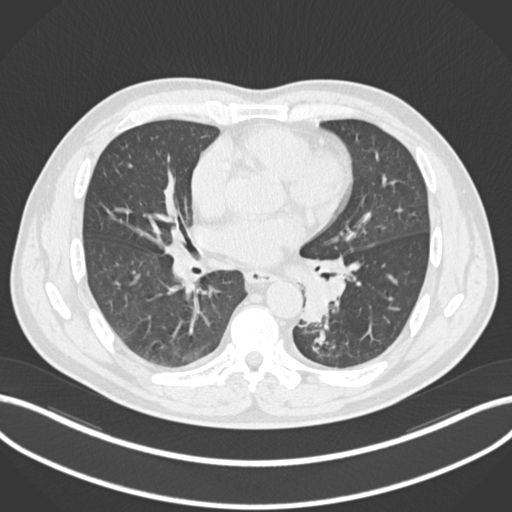
Chest CT, one axial slice. Slice 108 of 223 in the series (ordered by position). Reconstruction kernel B30f. 120 kVp. Lung window (W 1500 / L -600 HU). 512 × 512 image matrix. Patient: male, 50 years. Case-level facts recorded for this patient, not image findings: clinical TNM (as recorded): T2a N3 M0.
Annotated regions visible in this slice (bounding box drawn by a radiologist):
- lung tumour (recorded histology: squamous cell carcinoma): bounding box <297,270,347,323> (left, top, right, bottom; pixels)